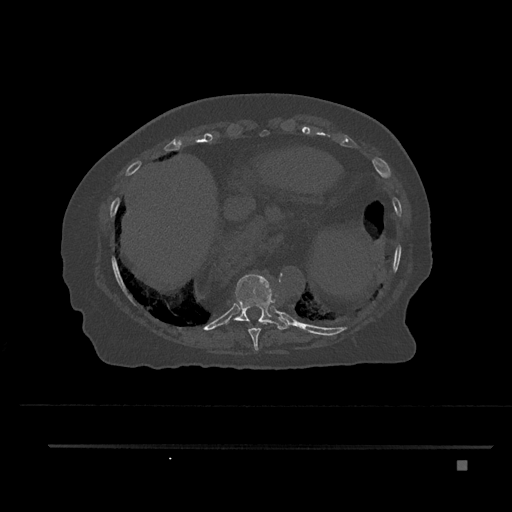
CT including the spine, one axial slice; slice 372 of 797 in the series (ordered by position); reconstruction kernel Br40s/3; 120 kVp; bone window (W 1800 / L 400 HU); 512 × 512 image matrix, field of view 437 × 437 mm. Patient: female, 76 years. Case-level facts recorded for this patient, not image findings: primary cancer: lung.
Outlined on this slice (semi-automatic segmentation, software-assisted and operator-edited):
- T10 vertebra: bounding box [x1, y1, x2, y2] px = [225, 274, 290, 329]
- T9 vertebra: [243, 320, 267, 351]